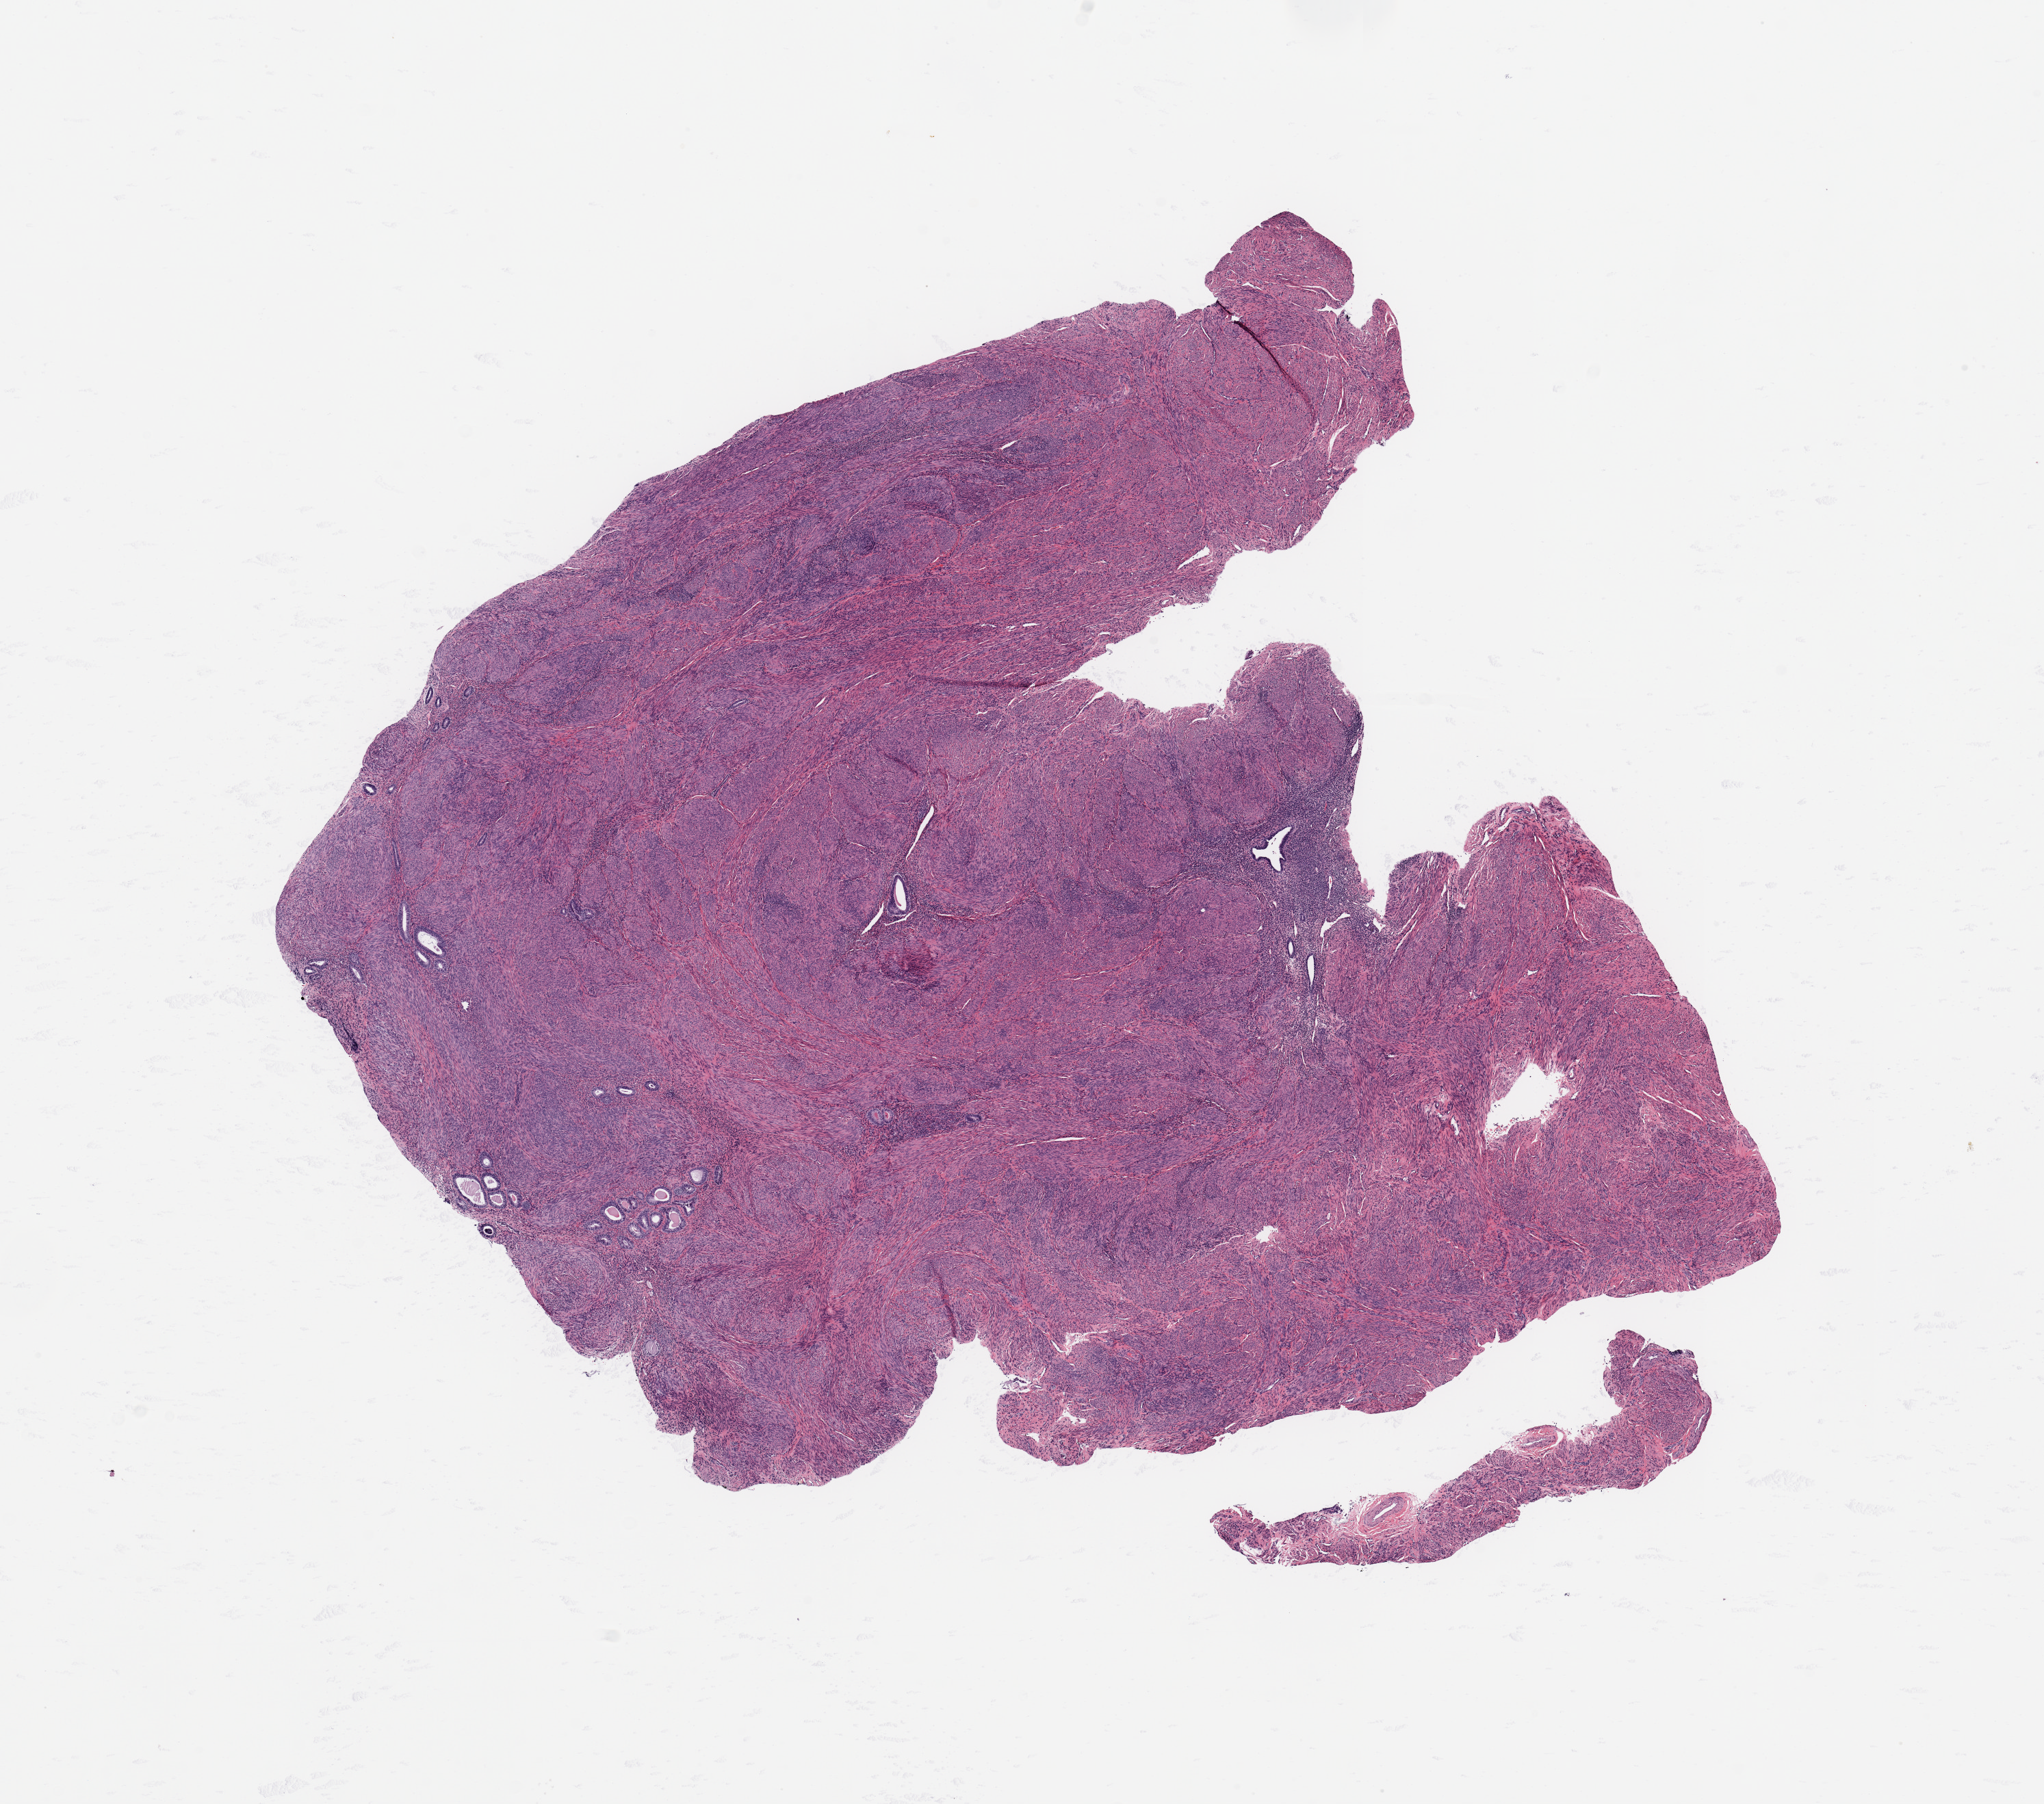
H&E whole-slide image — whole scanned area (about 11.8 x 10.4 mm, acquisition: 20x scan) shown as a low-resolution overview, normal (non-tumour) tissue sample, uterus. Patient: female, age 64 years.
This section: normal (non-tumour) tissue from the same patient. Patient diagnosis: Endometrioid adenocarcinoma, NOS.